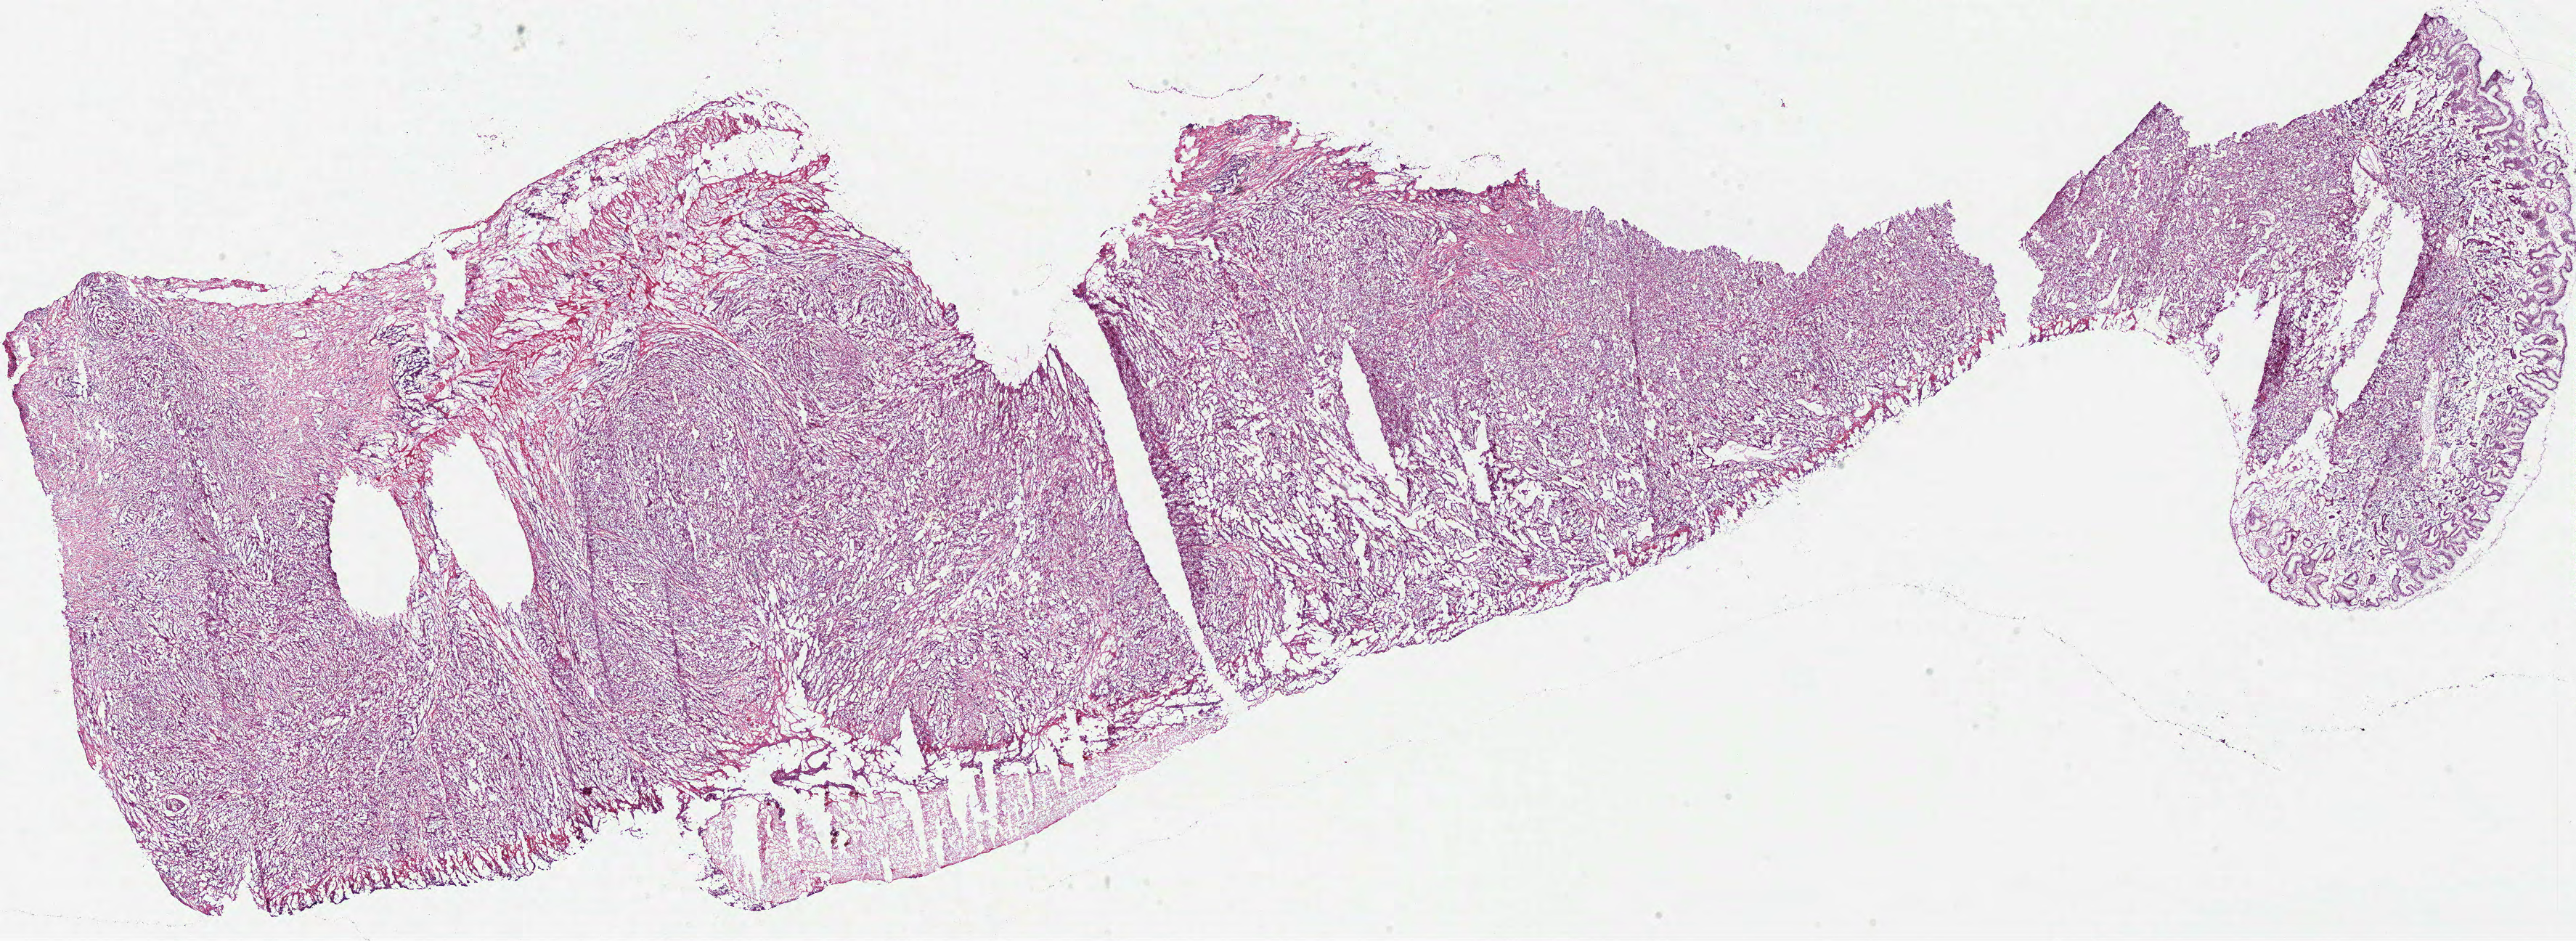
Whole-slide histology image, H&E — whole scanned area (about 27.9 x 10.2 mm, from a 40x scan) shown as a low-resolution overview. Frozen section from the bottom of the tissue portion. Stomach, primary tumour sample. Male, age 65 years at initial diagnosis. Histologic grade: G3 (poorly differentiated). Composition of this section per pathologist review: tumour cells 70%, tumour nuclei 75%, normal cells 10%, stromal cells 10%, necrosis 10%.
* pathologic diagnosis: Adenocarcinoma, NOS (body of stomach)
* AJCC pathologic stage: IIIA (7th edition)